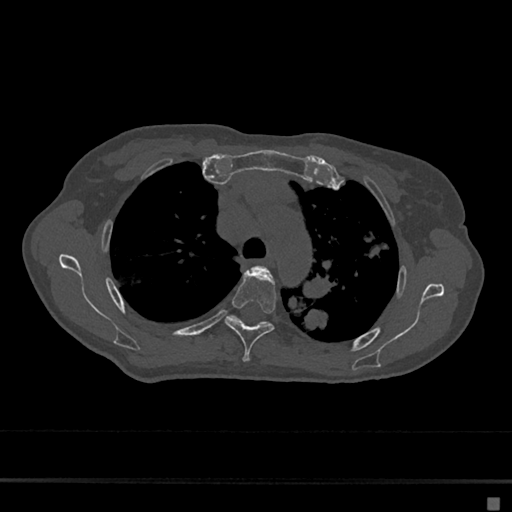
CT including the spine, one axial slice; slice 496 of 797 in the series (ordered by position); reconstruction kernel Br40s/3; 120 kVp; bone window (W 1800 / L 400 HU); 512 × 512 image matrix, field of view 360 × 360 mm. Patient: female, 68 years. From the clinical record (not read from this slice): primary cancer: renal.
Structures marked on this image (semi-automatically segmented with operator editing):
- T3 vertebra: bounding box <256,266,267,272> (left, top, right, bottom; pixels)
- T4 vertebra: <225,272,276,363>
- T5 vertebra: <228,315,269,327>